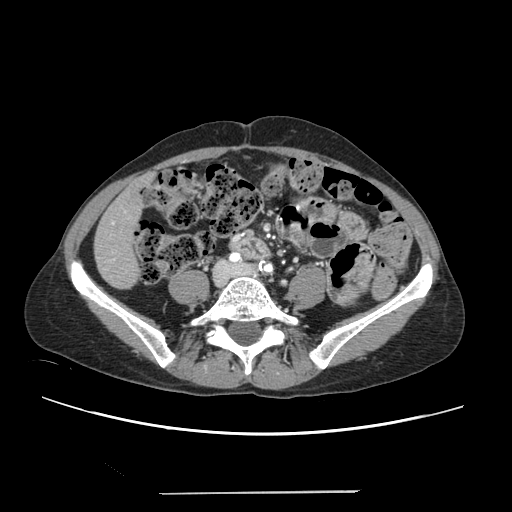
Contrast-enhanced abdominal CT, one axial slice; slice 31 of 240 in the series (ordered by position); 120 kVp; intravenous contrast given; soft-tissue window (W 400 / L 40 HU); 512 × 512 image matrix, field of view 371 × 371 mm. Female patient, age 60 years. Case-level facts recorded for this patient, not image findings: diagnosis: colorectal cancer liver metastases, imaged before liver resection; multiple liver metastases: no; largest metastasis: 1.5 cm; disease in both lobes: no.
Outlined on this slice (expert manual segmentation):
- liver: bounding box (x1, y1, x2, y2) in pixels: (95, 178, 148, 288)
- planned liver remnant (the part of the liver to remain after resection): (95, 178, 148, 288)
- portal vein (with intrahepatic branches): (112, 221, 115, 259)